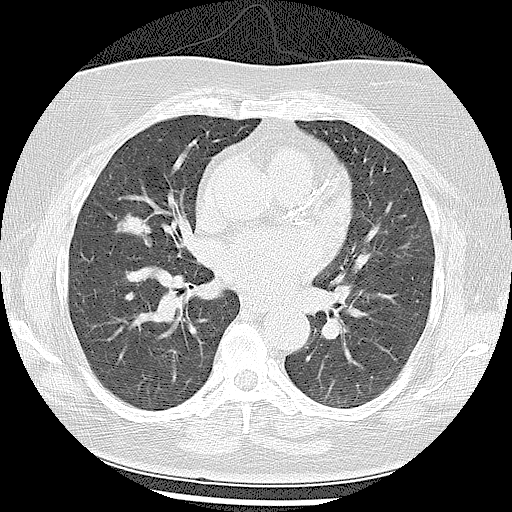
Low-dose screening chest CT, one axial slice. Position 50 of 102 along the scan axis. Reconstruction kernel LUNG. Lung window (W 1500 / L -600 HU). 2.5 mm slice thickness. 512 × 512 image matrix, field of view 350 × 350 mm.
Annotated regions visible in this slice (manually delineated by an expert):
- lesion 1 (tumor, middle lobe of right lung): bounding box [x1, y1, x2, y2] px = [115, 212, 152, 247]